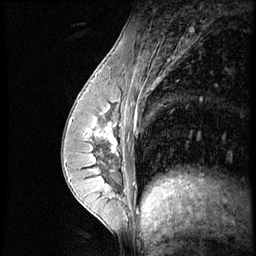
Breast MRI (dynamic contrast-enhanced), one sagittal slice; slice 23 of 56 in the series (ordered by position); dynamic contrast-enhanced series, image 2 of 4 at this slice position (ordered by acquisition); 1.5 T; TE 4.2 ms, TR 8.9 ms; 256 × 256 image matrix, field of view 200 × 200 mm. Patient: female, 35 years. From the clinical record (not read from this slice): setting: breast cancer imaged before/during neoadjuvant chemotherapy; receptor status: HER2-positive.
Structures marked on this image (semi-automatic segmentation, software-assisted and operator-edited):
- analysis volume of interest (the breast-tissue region the enhancement analysis was run in; not a lesion): bounding box <73,111,131,164> (left, top, right, bottom; pixels)
- tumour enhancement mask (voxels above the 140 % enhancement threshold inside the analysis volume of interest): <82,118,118,152>